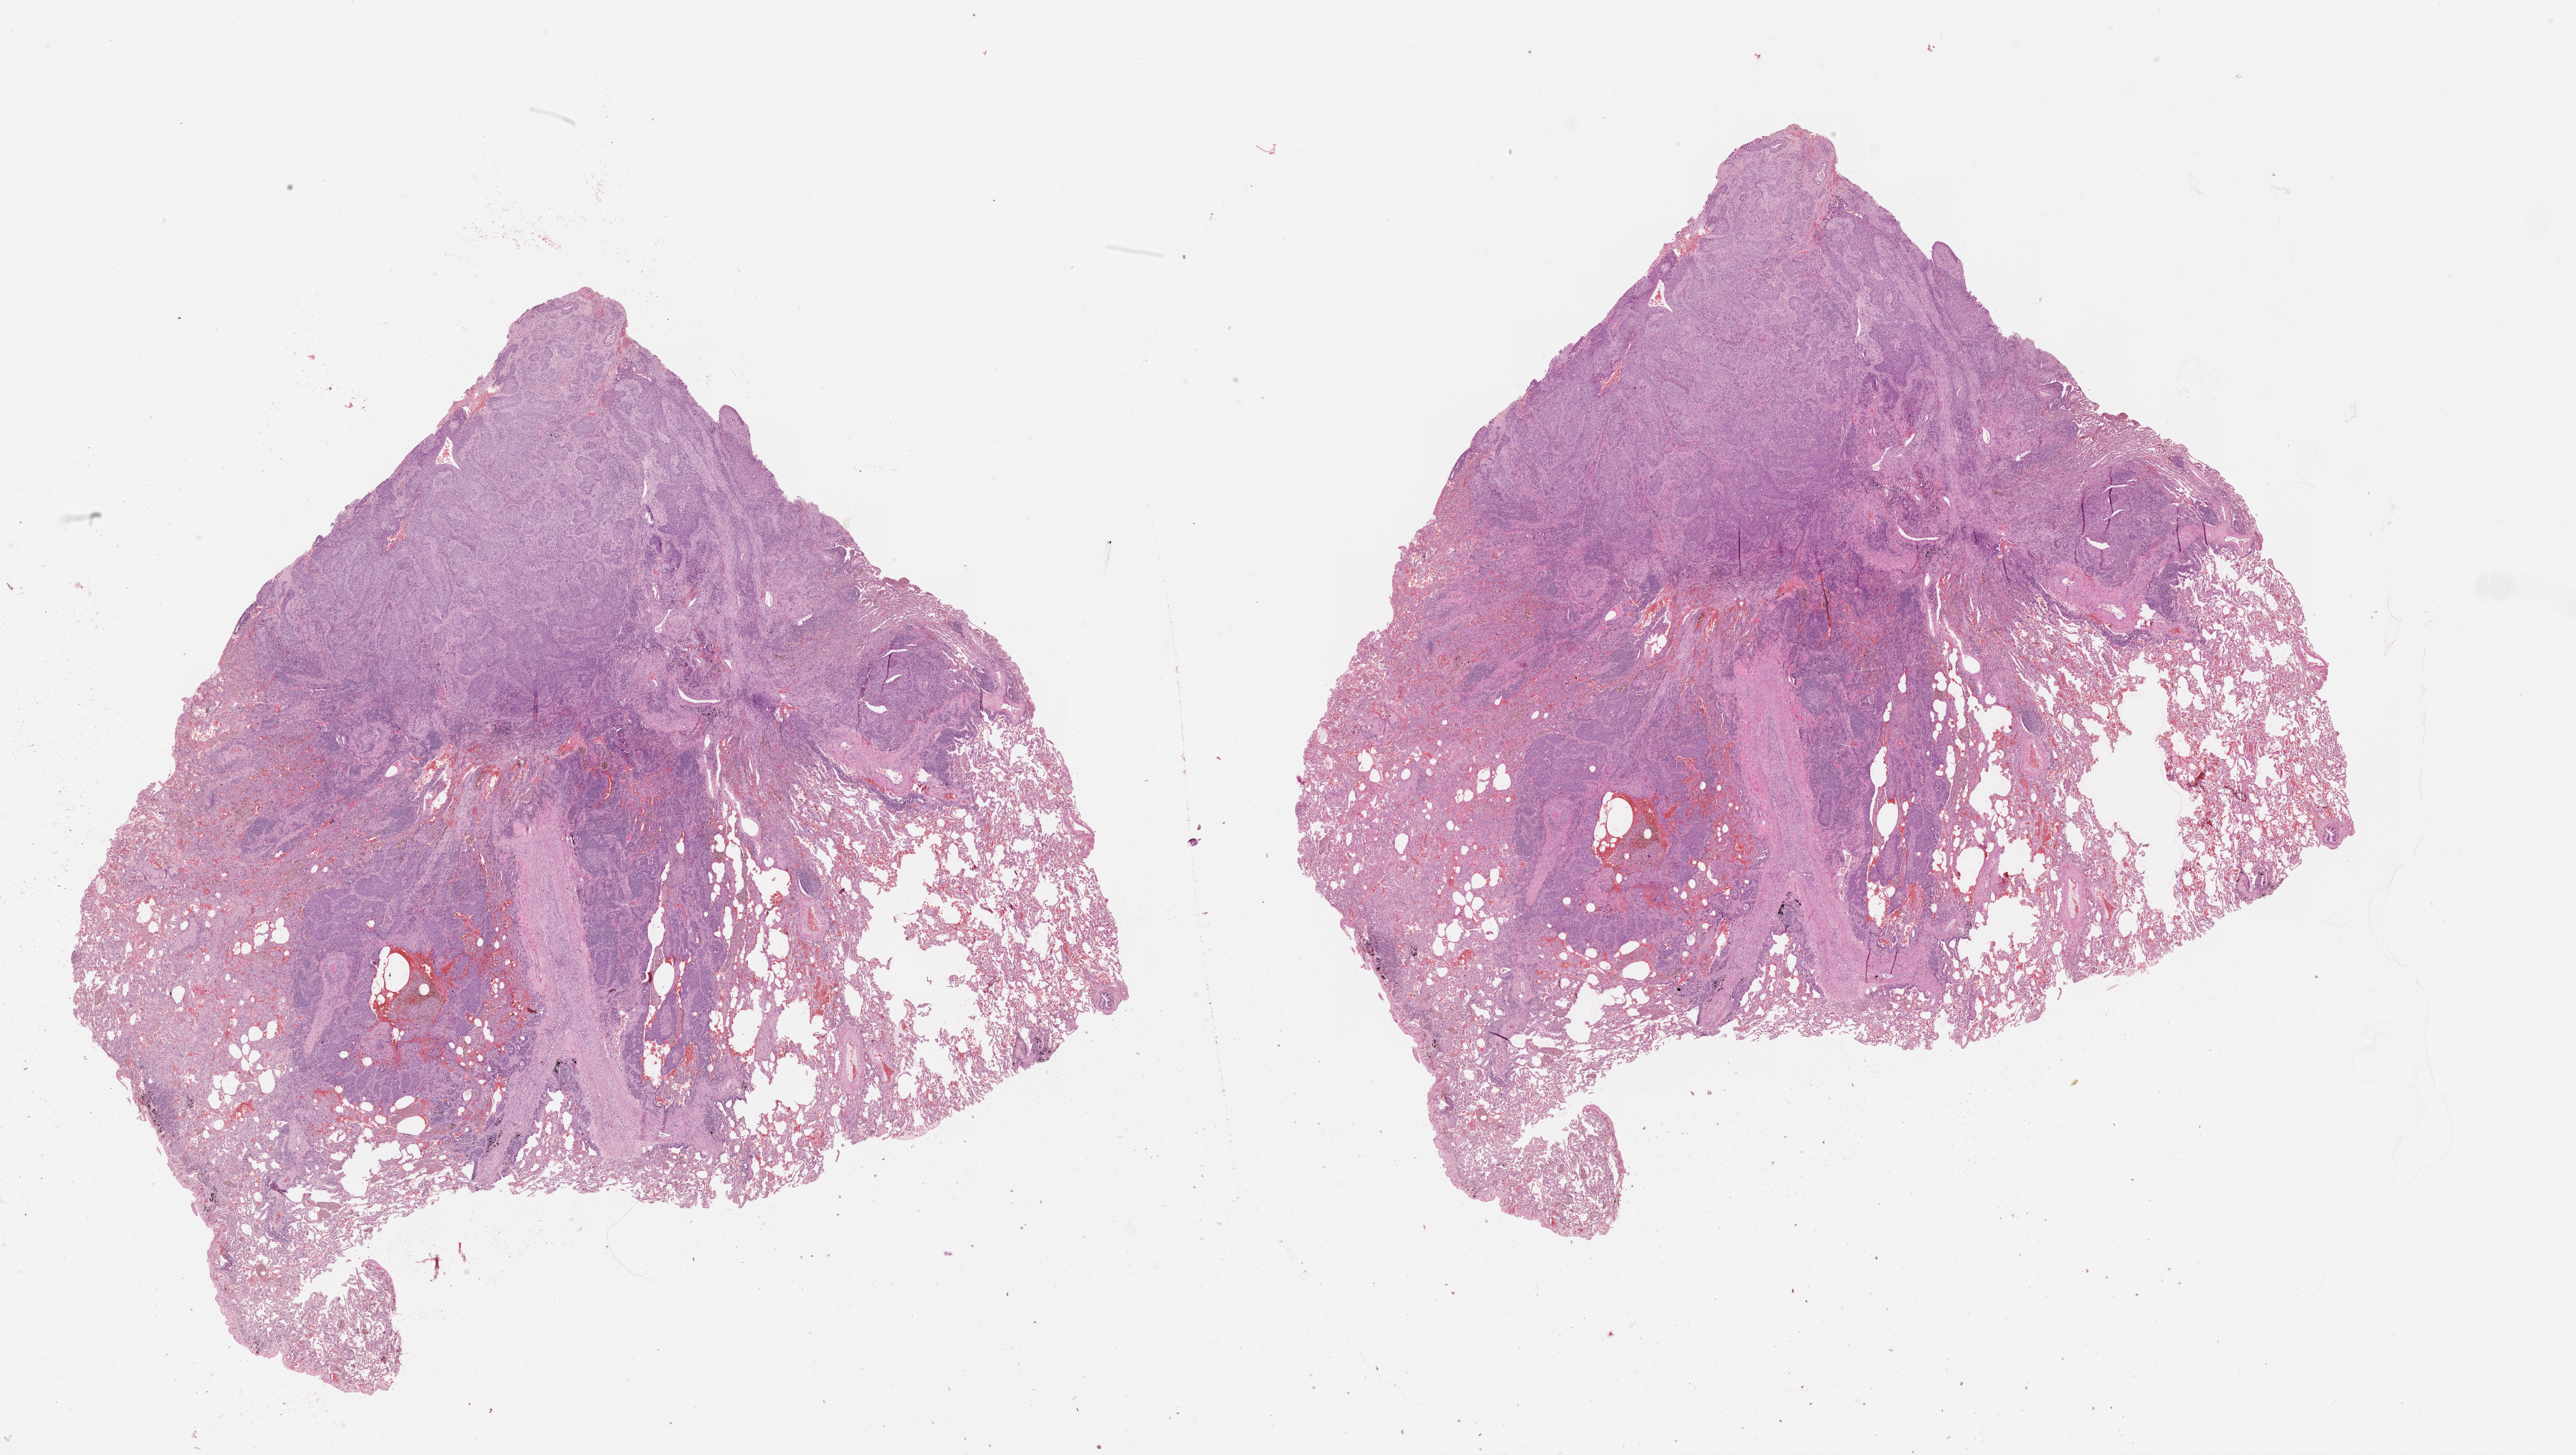
Digitized H&E-stained tissue section (whole slide), shown as a low-resolution overview of the whole scanned area (about 29.1 x 16.4 mm, slide scanned at 20x); lung, tumour tissue. Patient: male, age 69 years.
Patient diagnosis (cohort enrolment): squamous cell carcinoma (lung).